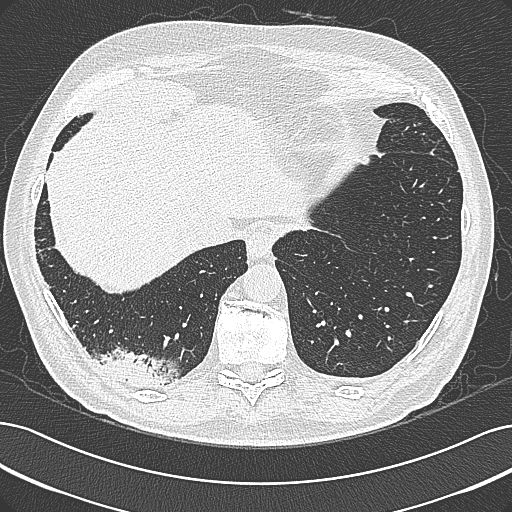
Chest CT (low-dose screening protocol), one axial image, baseline annual screen, lung window (W 1500 / L -600 HU), 1 mm slice thickness. Male participant, aged 68 years at enrolment. Former smoker at enrolment.
Lesion marked by an expert reader, box from (x=96, y=340) to (x=186, y=401) px. No non-calcified nodule or mass ≥4 mm was recorded by the screening reader at this exam. Official screen result: negative screen, significant abnormalities not suspicious for lung cancer. Later outcome: lung cancer diagnosed 154 days after this screen — mucinous adenocarcinoma, right lower lobe, well differentiated (G1), stage IB (AJCC 6th edition), 50 mm at pathology.